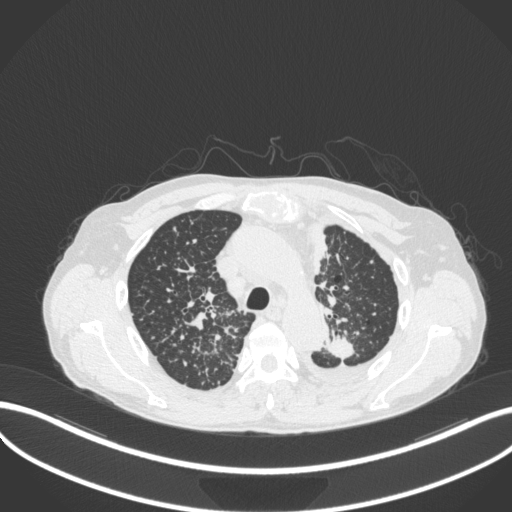
Chest CT, one axial slice. Position 260 of 319 along the scan axis. Reconstruction kernel B31f. 120 kVp. Lung window (W 1500 / L -600 HU). 1 mm slice thickness. 512 × 512 image matrix, field of view 400 × 400 mm. Male patient, age 58 years. From the clinical record (not read from this slice): clinical TNM (as recorded): T1c N3 M1.
Annotated regions visible in this slice (bounding box drawn by a radiologist):
- lung tumour (recorded histology: adenocarcinoma): bounding box [x1, y1, x2, y2] px = [323, 335, 358, 359]